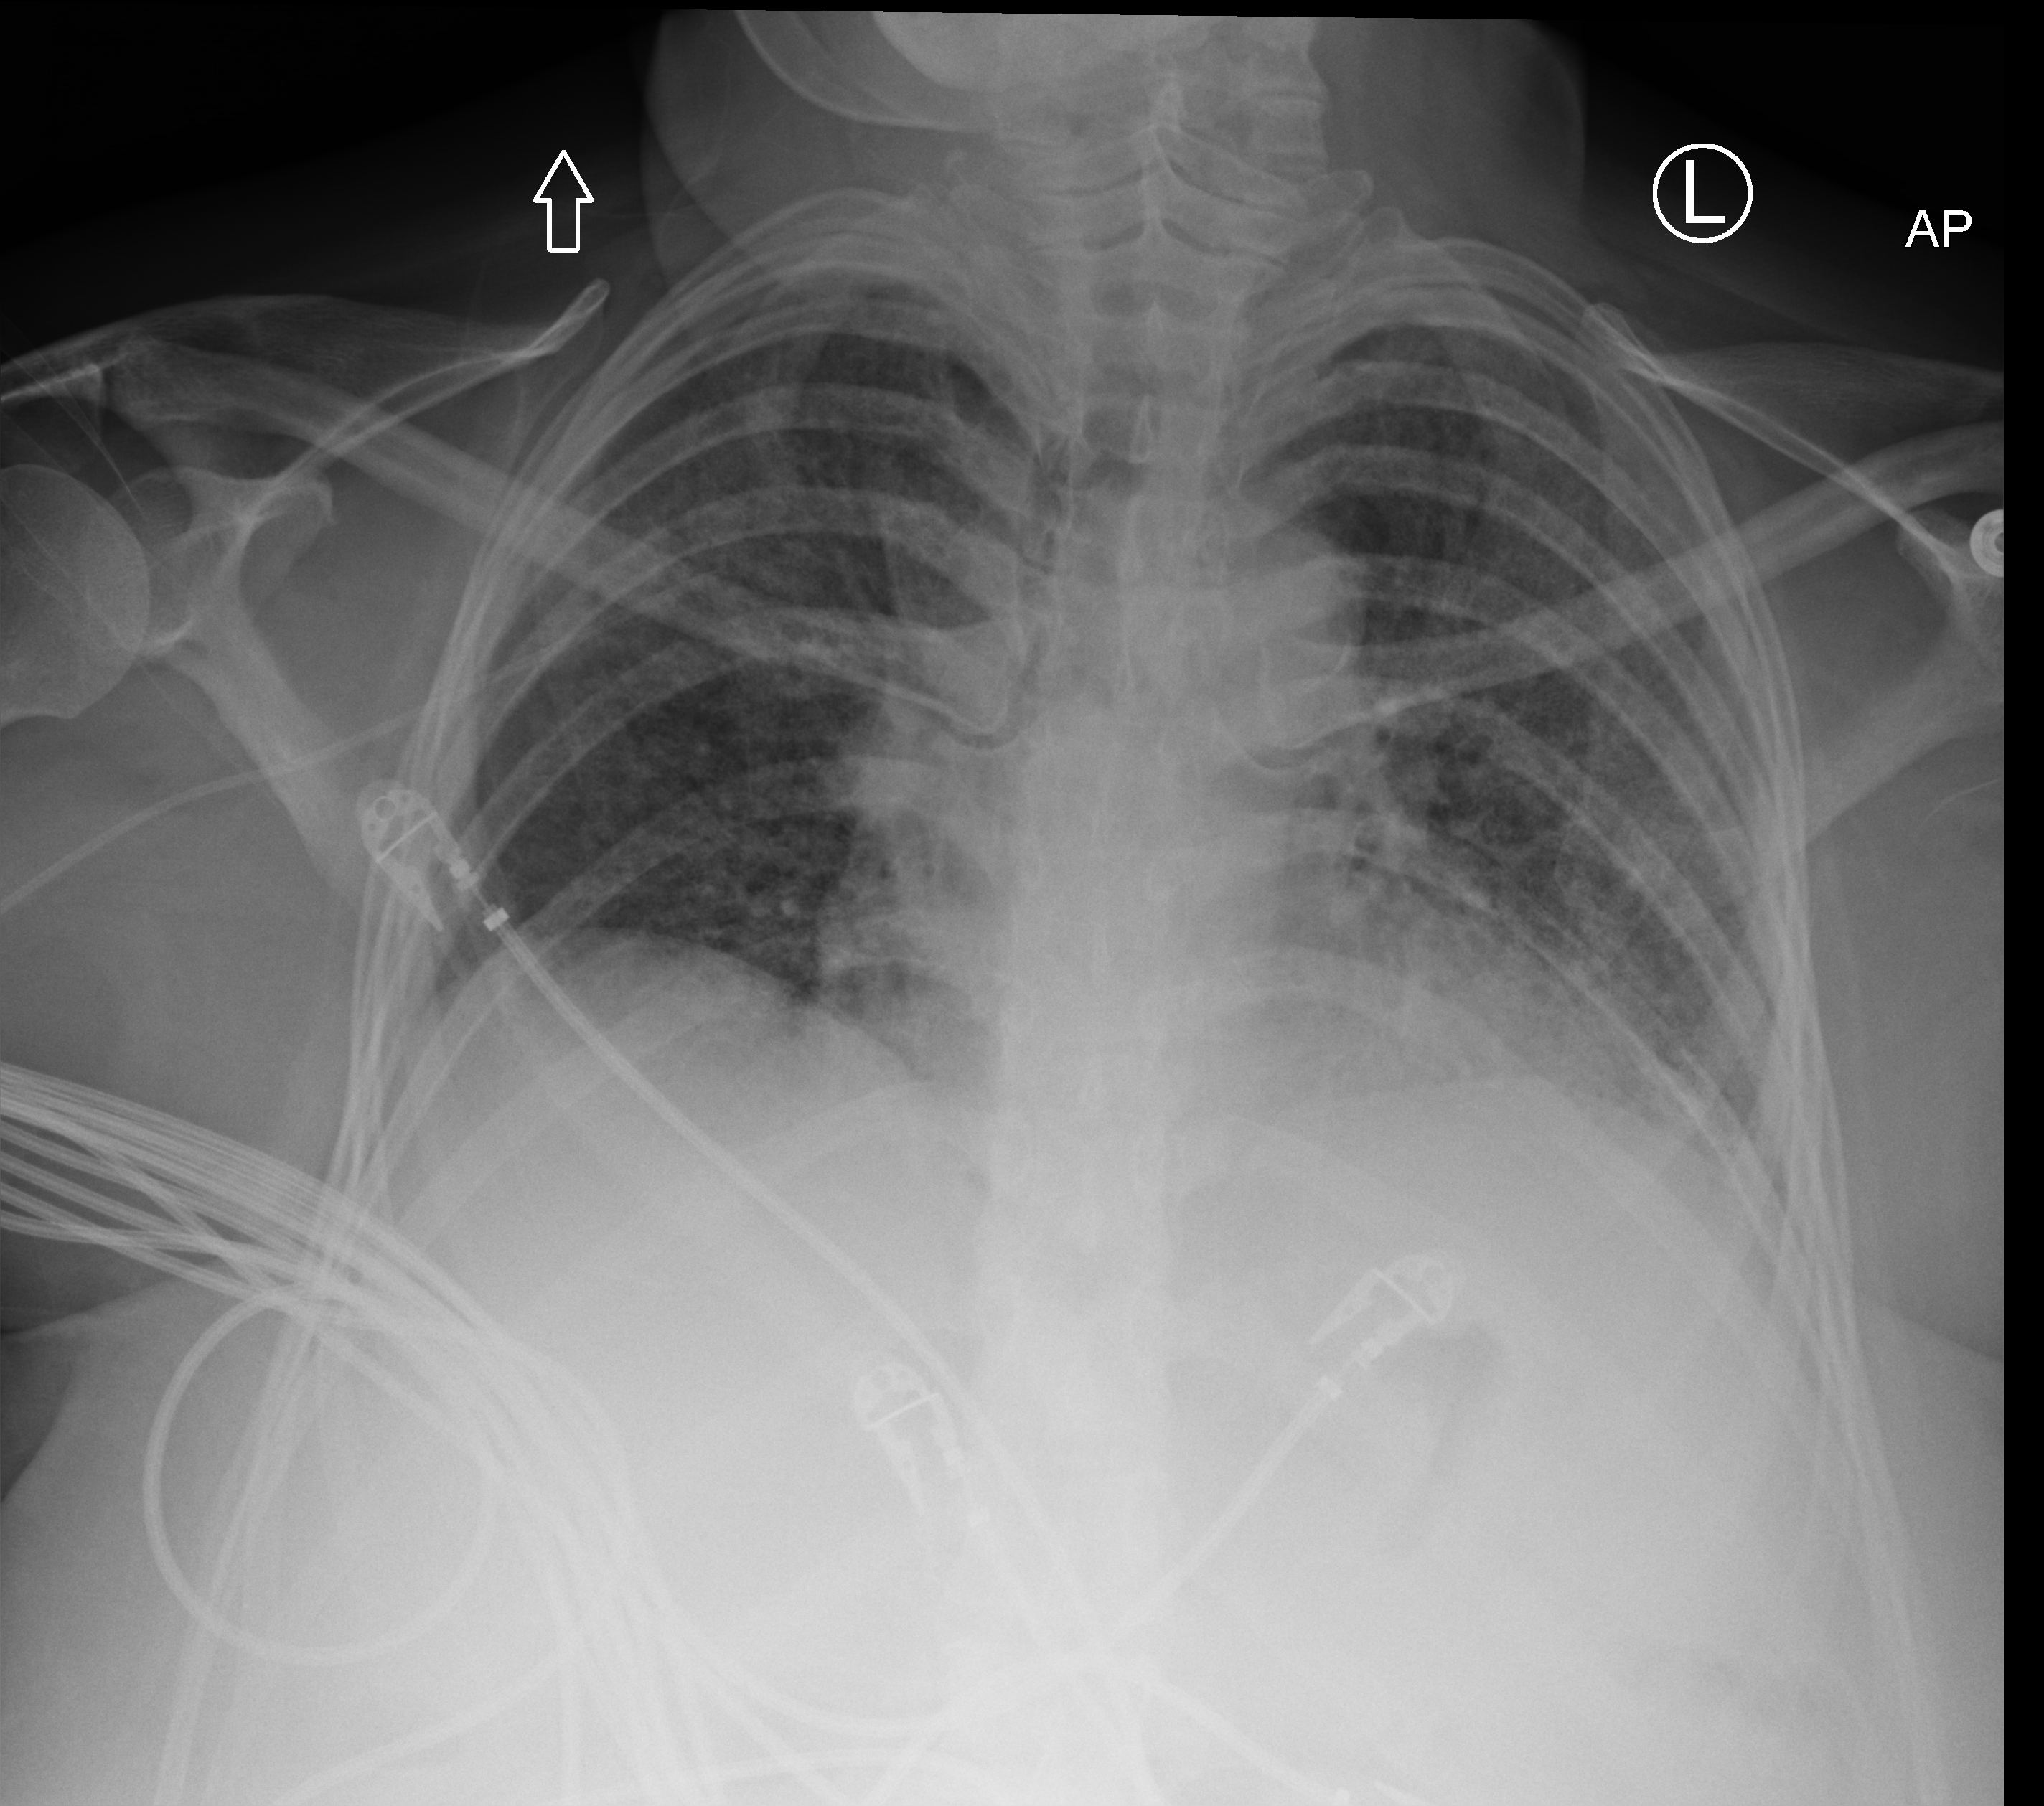
Chest X-ray (portable); anteroposterior (AP) projection. Female patient hospitalised with COVID-19, age 18–59 years.
Admission-level facts for this patient (not findings on this image; timing relative to this image not recorded): admitted to intensive care during this hospital stay: yes.